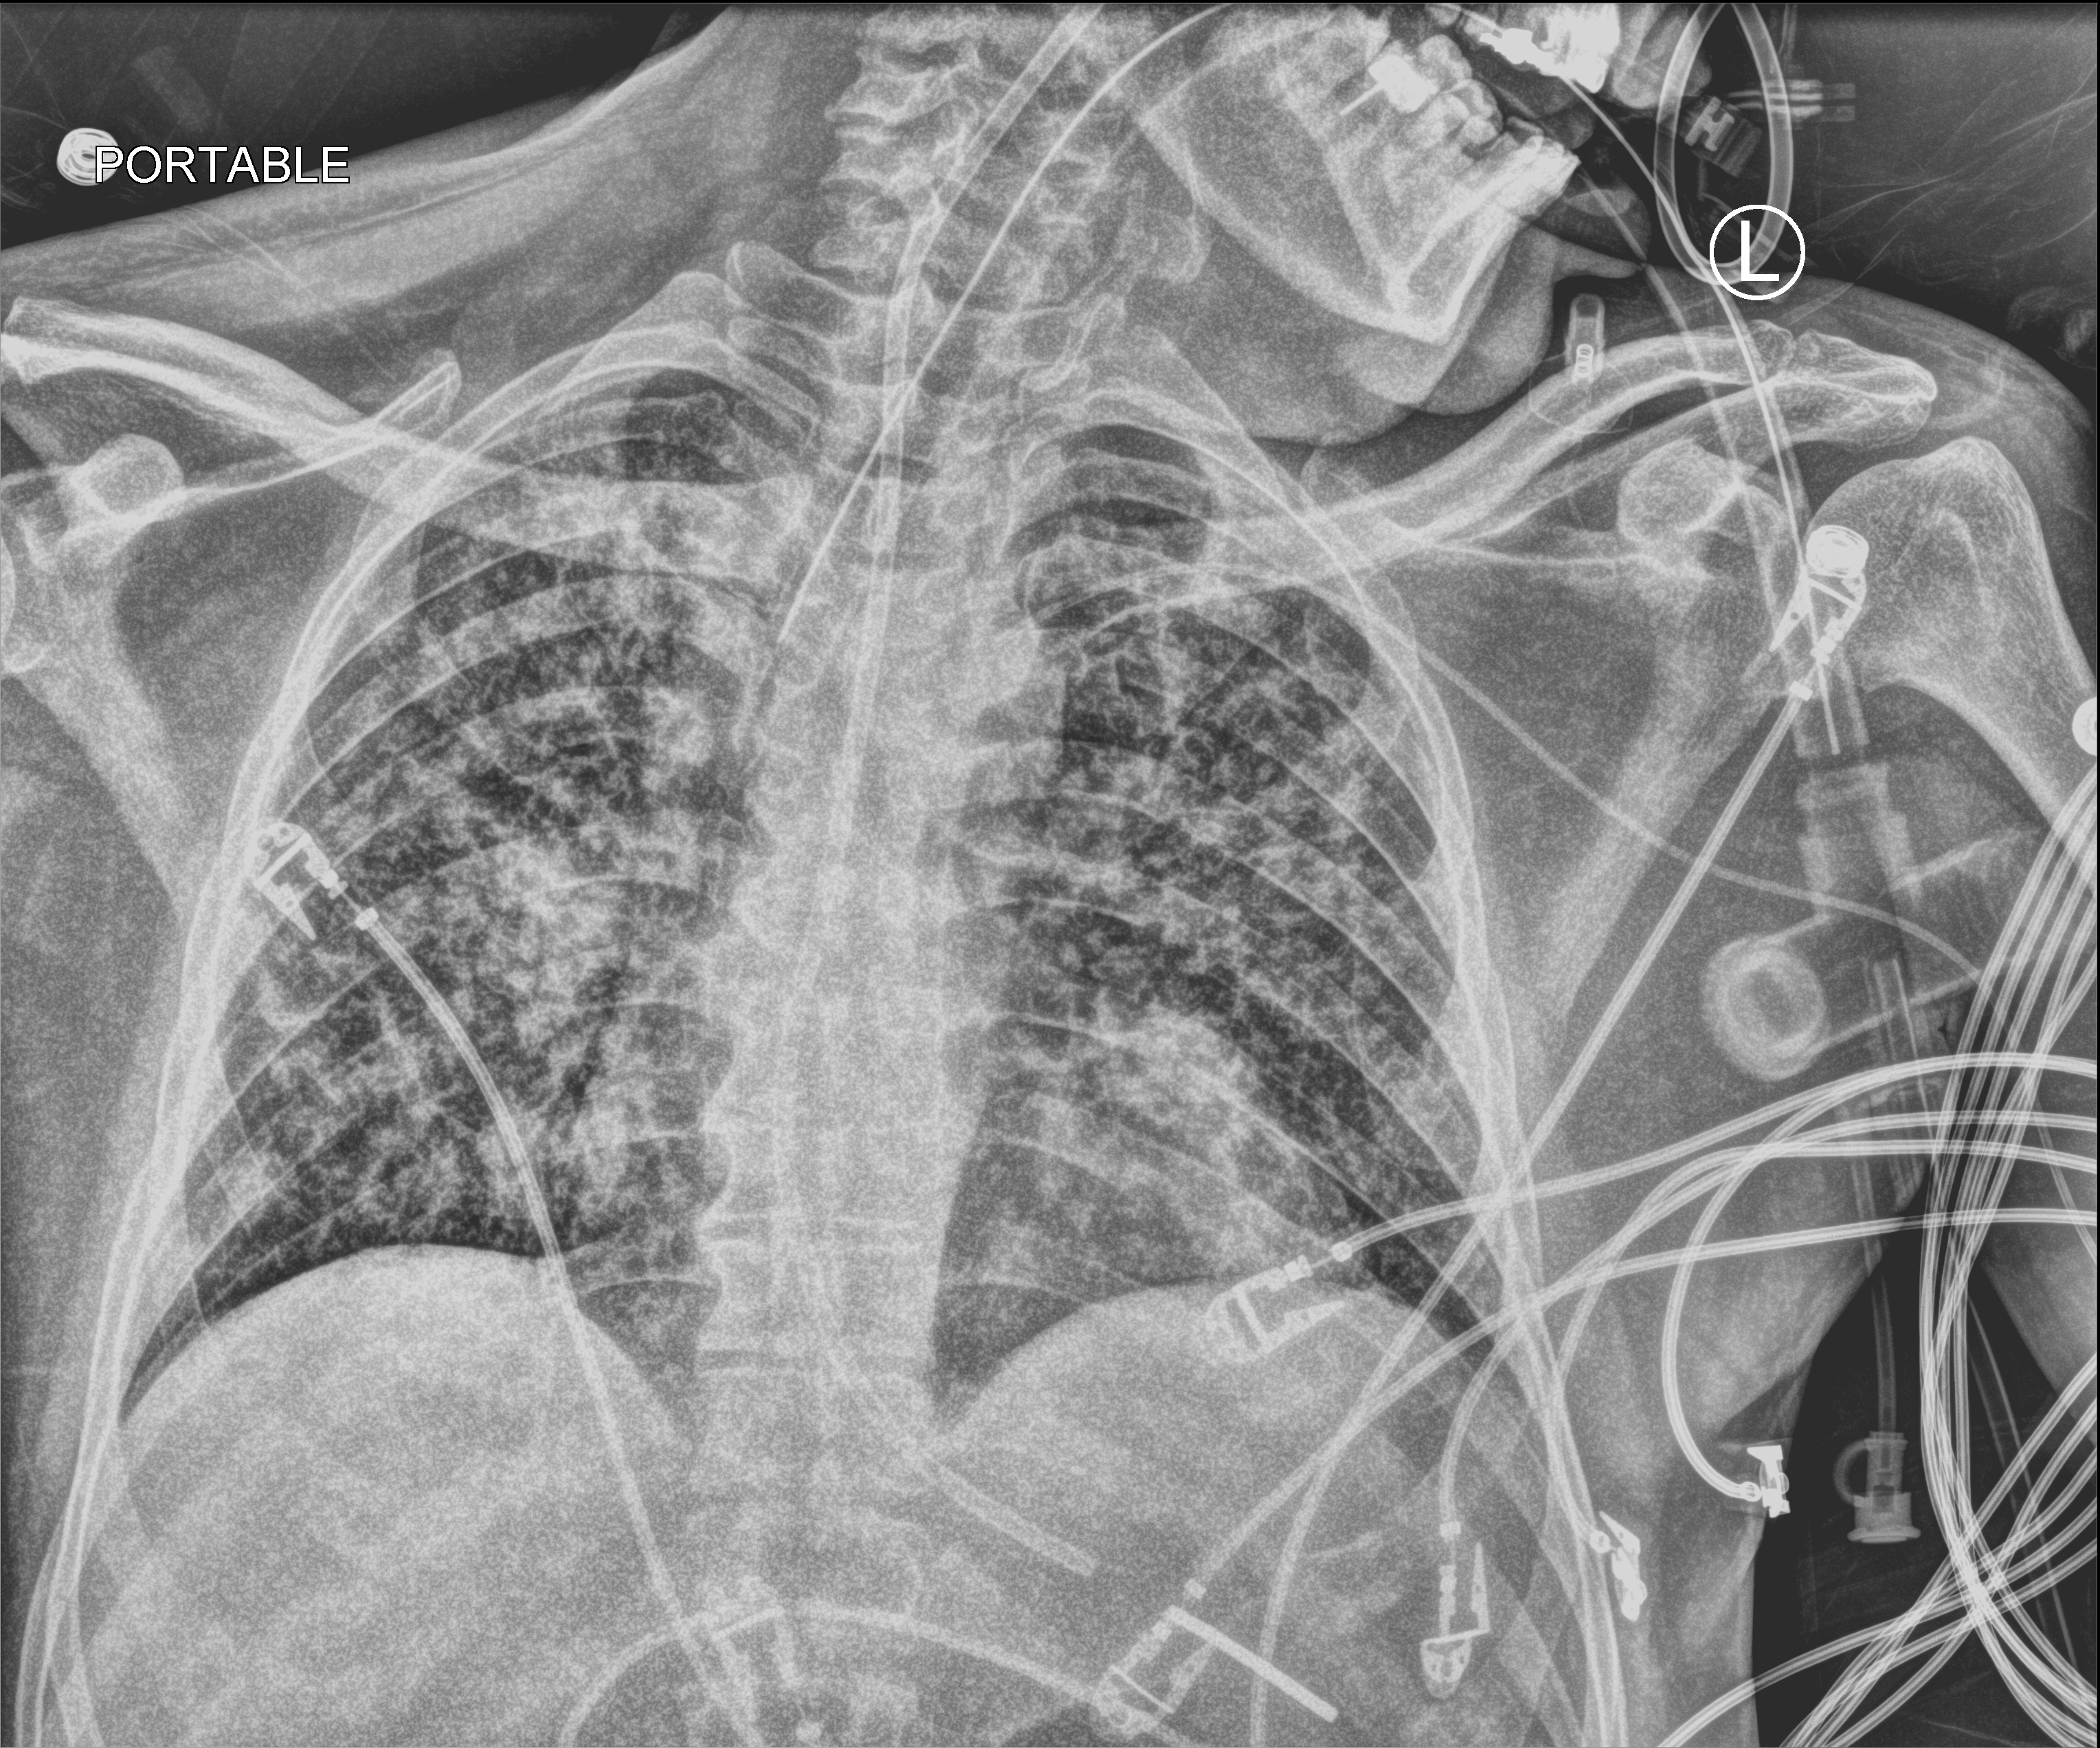
Chest X-ray (portable); anteroposterior (AP) projection. Male patient hospitalised with COVID-19, age 18–59 years.
From the hospital-stay record, not from the radiograph (when in the stay this image was taken is not recorded): hypertension (admission record): yes.